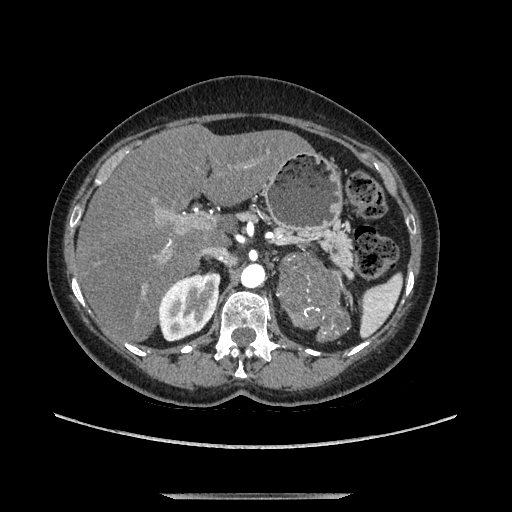
Contrast-enhanced abdominal CT, one axial slice. Position 77 of 169 along the scan axis. Soft-tissue window (W 400 / L 40 HU). 1.25 mm slice thickness. 512 × 512 image matrix. Female patient. Case-level facts recorded for this patient, not image findings: diagnosis: adrenocortical carcinoma; tumour side: left adrenal; tumour size at pathology: 9 cm; Ki-67 index: 2 %; stage (as recorded): 3.
Structures marked on this image (semi-automatically segmented with operator editing):
- mass: bounding box (x1, y1, x2, y2) in pixels: (279, 257, 344, 340)